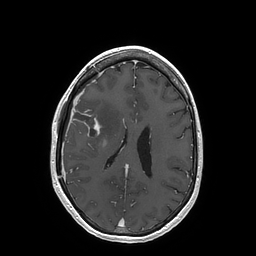
Brain MRI from a brain-tumour surgery series, one axial slice. Position 68 of 202 along the scan axis. T1-weighted post-contrast. 256 × 256 image matrix, field of view 250 × 250 mm. From the clinical record (not read from this slice): histopathology: Glioblastoma; WHO grade: 4; IDH mutation: no; tumour location: Right Insular.
Annotated regions visible in this slice (manually delineated by an expert):
- tumour: bounding box [x1, y1, x2, y2] px = [71, 108, 100, 137]